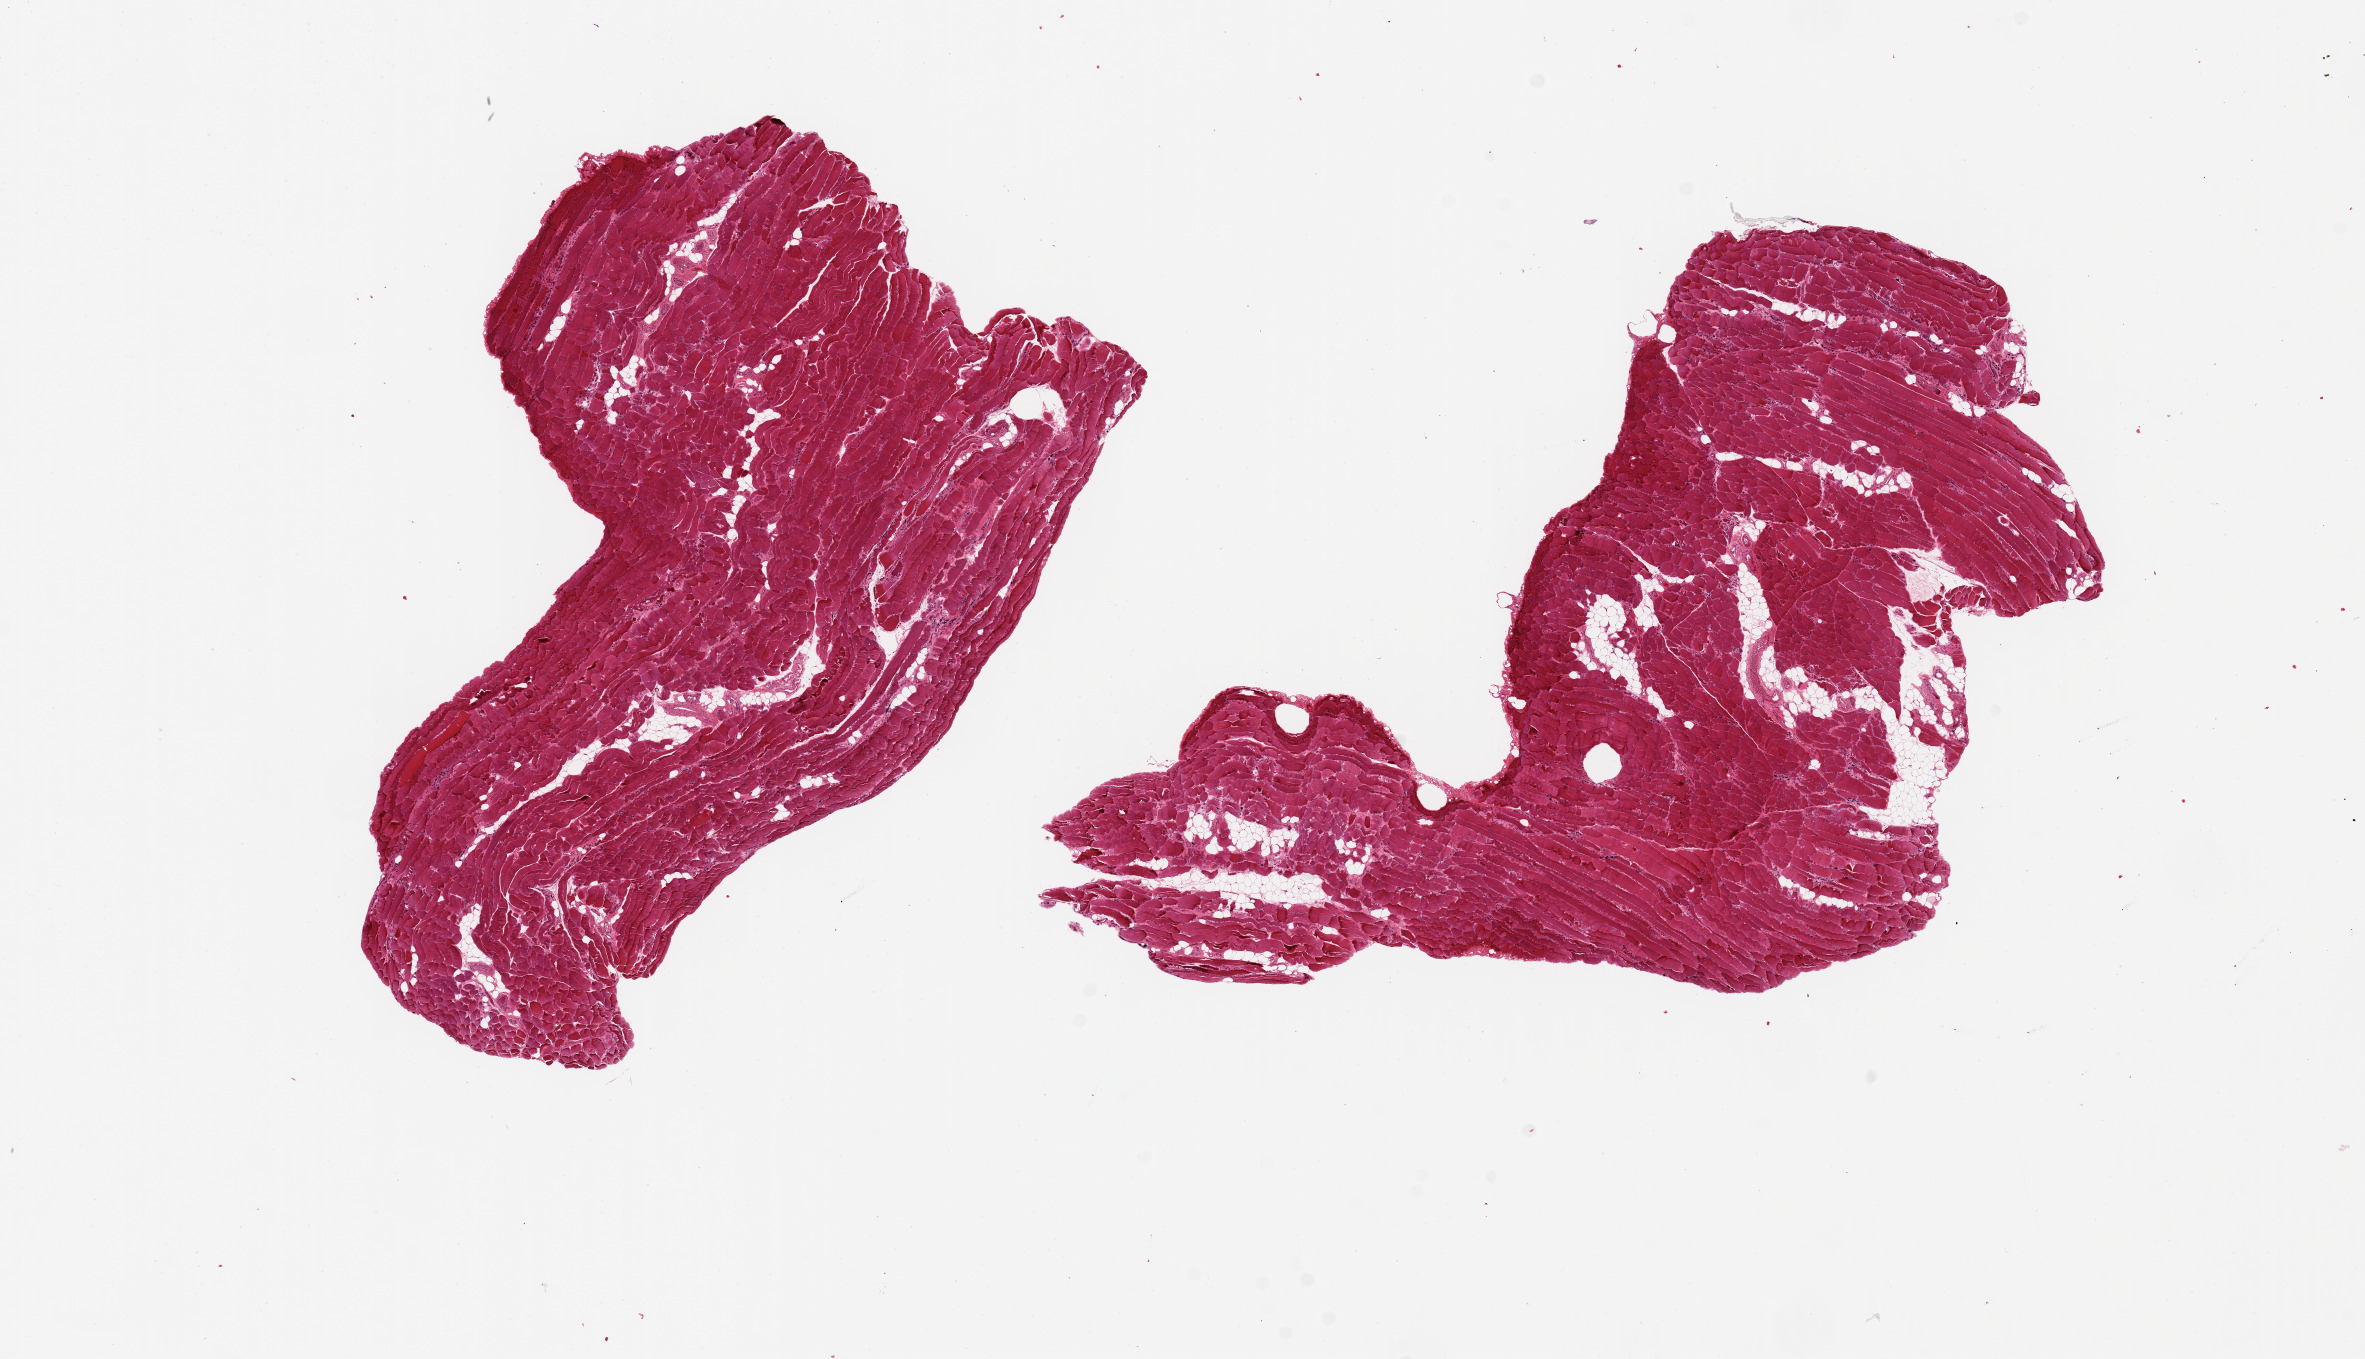
Whole-slide image, hematoxylin and eosin (H&E) stain — shown as a low-resolution overview of the whole scanned area (about 18.7 x 10.7 mm, acquisition: 20x scan), PAXgene-fixed, paraffin-embedded tissue, target tissue: skeletal muscle, donor tissue sample. Donor sex: male.
- pathologist's review note for this sample: 2 pieces, 7x5 & 8x6mm; Well trimmed; <10% internal adipose